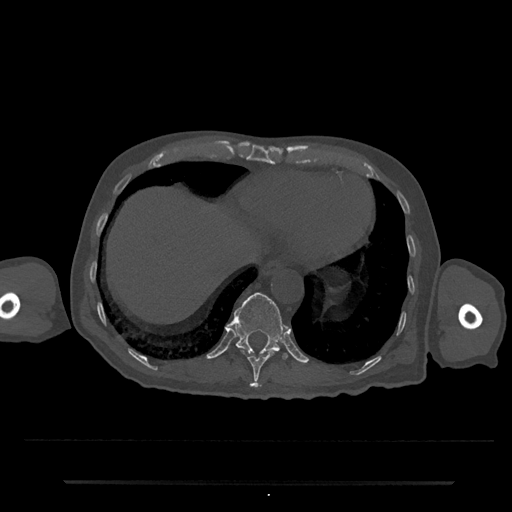
CT including the spine, one axial slice. Position 281 of 797 along the scan axis. 120 kVp. Bone window (W 1800 / L 400 HU). 0.5 mm slice thickness. 512 × 512 image matrix, field of view 427 × 427 mm. Patient: male, 74 years. Case-level facts recorded for this patient, not image findings: primary cancer: prostate.
Annotated regions visible in this slice (semi-automatic segmentation, software-assisted and operator-edited):
- T10 vertebra: bounding box (x1, y1, x2, y2) in pixels: (240, 350, 277, 388)
- T11 vertebra: (227, 292, 288, 359)